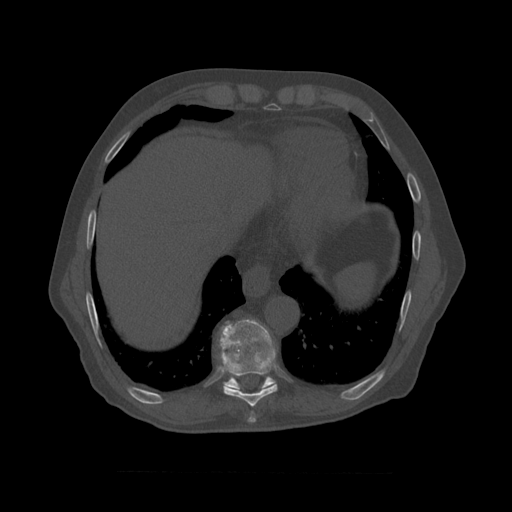
CT including the spine, one axial slice. Position 439 of 450 along the scan axis. 120 kVp. Bone window (W 1800 / L 400 HU). 1.25 mm slice thickness. 512 × 512 image matrix, field of view 405 × 405 mm. Patient age 75 years. Case-level facts recorded for this patient, not image findings: primary cancer: prostate.
Outlined on this slice (semi-automatic segmentation, software-assisted and operator-edited):
- T8 vertebra: box from (x=219, y=329) to (x=278, y=407) px
- T9 vertebra: (x=221, y=319)–(x=277, y=389)